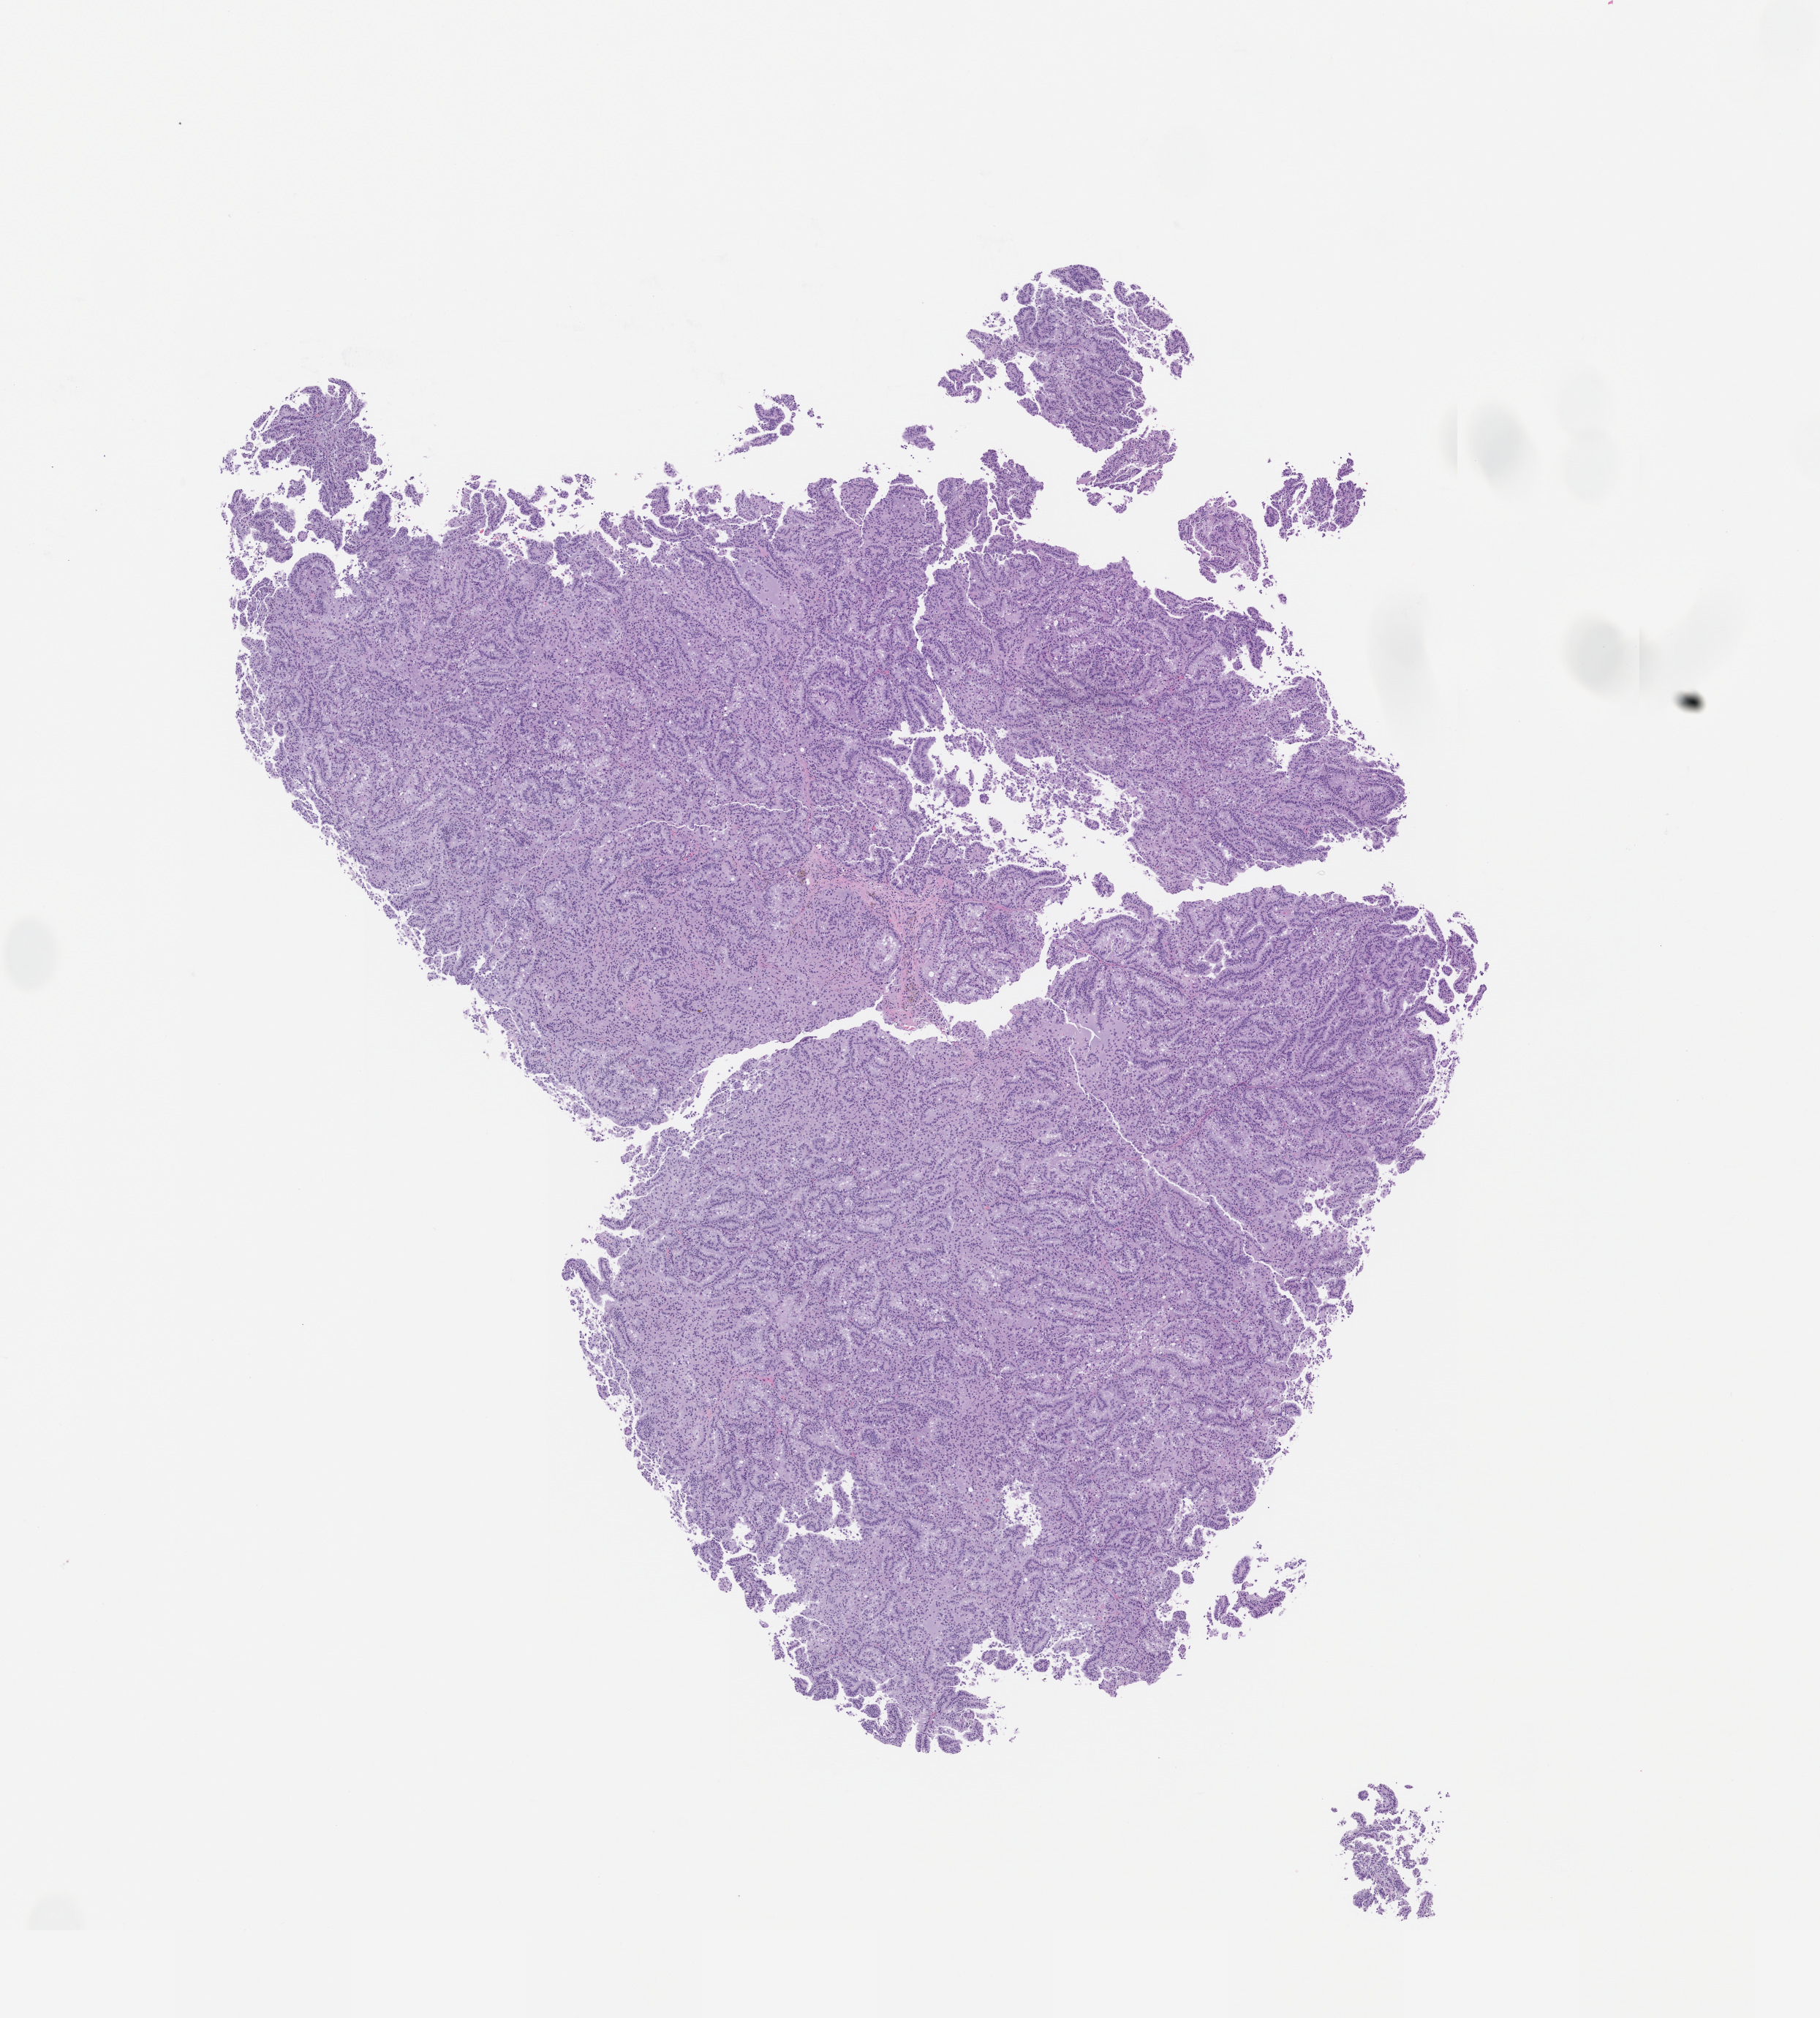
H&E whole-slide image of a patient-derived xenograft (PDX) tumor grown in a mouse, passage 2 — low-resolution overview of the scanned area, about 10.0 x 11.1 mm. Formalin-fixed paraffin-embedded section. Originating tumor site category: genitourinary tract.
Originating patient diagnosis: Renal Cell Carcinoma, Not Otherwise Specified.